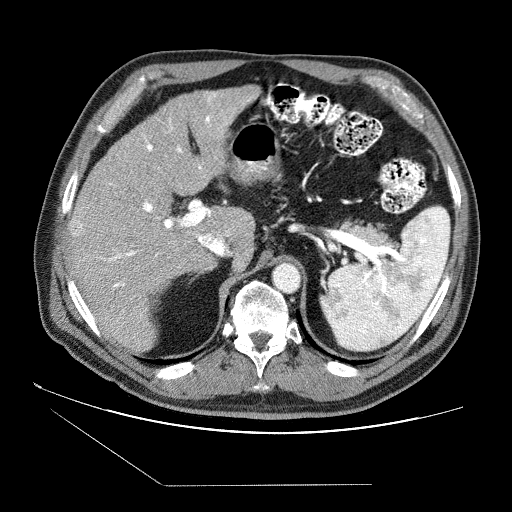
Contrast-enhanced abdominal CT (liver protocol), one axial slice; position 51 of 87 along the scan axis; 120 kVp; soft-tissue window (W 400 / L 40 HU); 2.5 mm slice thickness; 512 × 512 image matrix, field of view 400 × 400 mm. From the clinical record (not read from this slice): diagnosis: hepatocellular carcinoma (patient treated with transarterial chemoembolisation; whether this scan precedes or follows treatment is not stated here); TNM stage (as recorded): Stage-II; Child-Pugh class: B; tumour differentiation: no biopsy; tumour size: 2.6 cm.
Outlined on this slice (semi-automatically segmented with operator editing):
- liver parenchyma outside the tumour (the mass and vessels are separate outlines, so this box may not span the whole liver): box from (x=68, y=86) to (x=258, y=352) px
- mass: (x=69, y=218)–(x=82, y=234)
- liver vessels: (x=100, y=93)–(x=250, y=322)